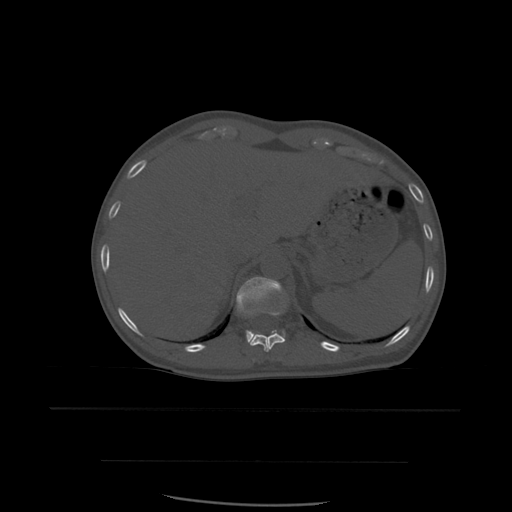
CT including the spine, one axial slice; position 288 of 574 along the scan axis; bone window (W 1800 / L 400 HU); 512 × 512 image matrix. Patient age 48 years. Case-level facts recorded for this patient, not image findings: primary cancer: lung; vertebrae with lytic lesions (as recorded): T11.
Outlined on this slice (semi-automatically segmented with operator editing):
- T11 vertebra: bounding box (x1, y1, x2, y2) in pixels: (247, 308, 286, 352)
- T12 vertebra: (237, 277, 285, 343)